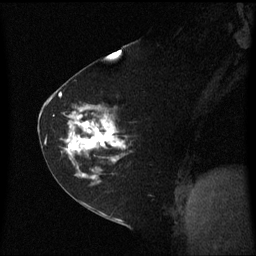
Breast MRI (dynamic contrast-enhanced), one sagittal slice. Position 37 of 60 along the scan axis. Dynamic contrast-enhanced series, image 2 of 3 at this slice position (ordered by acquisition). 1.5 T. TE 4.2 ms, TR 8.4 ms. 2 mm slice thickness. 256 × 256 image matrix. Patient: female, 60 years. Case-level facts recorded for this patient, not image findings: setting: breast cancer imaged before/during neoadjuvant chemotherapy; receptor status: triple-negative.
Structures marked on this image (semi-automatically segmented with operator editing):
- analysis volume of interest (the breast-tissue region the enhancement analysis was run in; not a lesion): bounding box <45,99,130,182> (left, top, right, bottom; pixels)
- tumour enhancement mask (voxels above the 70 % enhancement threshold inside the analysis volume of interest): <51,100,127,181>